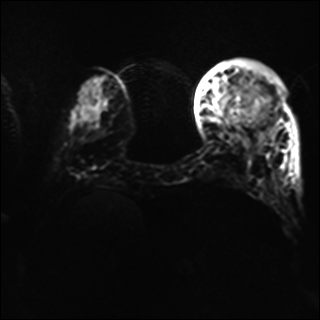
Breast MRI, one axial slice. Slice 13 of 40 in the series (ordered by position). Diffusion-weighted series; image 2 of 4 stored at this slice position (different b-values; order by instance number). 1.5 T. 4 mm slice thickness. 320 × 320 image matrix. Female patient.
Annotated regions visible in this slice (expert manual segmentation):
- tumour on diffusion-weighted imaging: bounding box <227,89,265,121> (left, top, right, bottom; pixels)